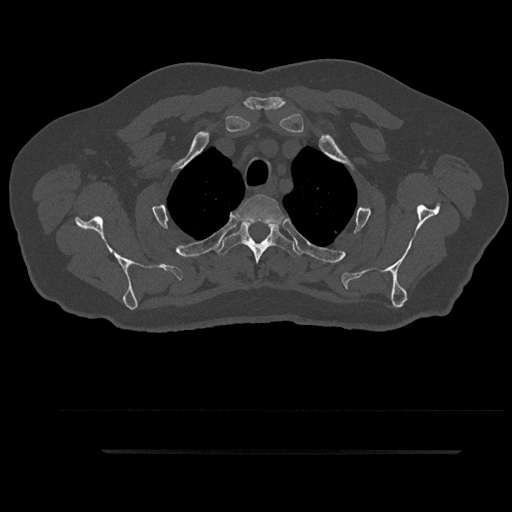
CT including the spine, one axial slice; position 731 of 797 along the scan axis; 120 kVp; bone window (W 1800 / L 400 HU); 0.5 mm slice thickness; 512 × 512 image matrix, field of view 432 × 432 mm. Patient: male, 63 years. From the clinical record (not read from this slice): primary cancer: renal; vertebrae with lytic lesions (as recorded): T8.
Structures marked on this image (semi-automatically segmented with operator editing):
- T2 vertebra: bounding box <236,194,284,224> (left, top, right, bottom; pixels)
- T3 vertebra: <215,220,302,264>